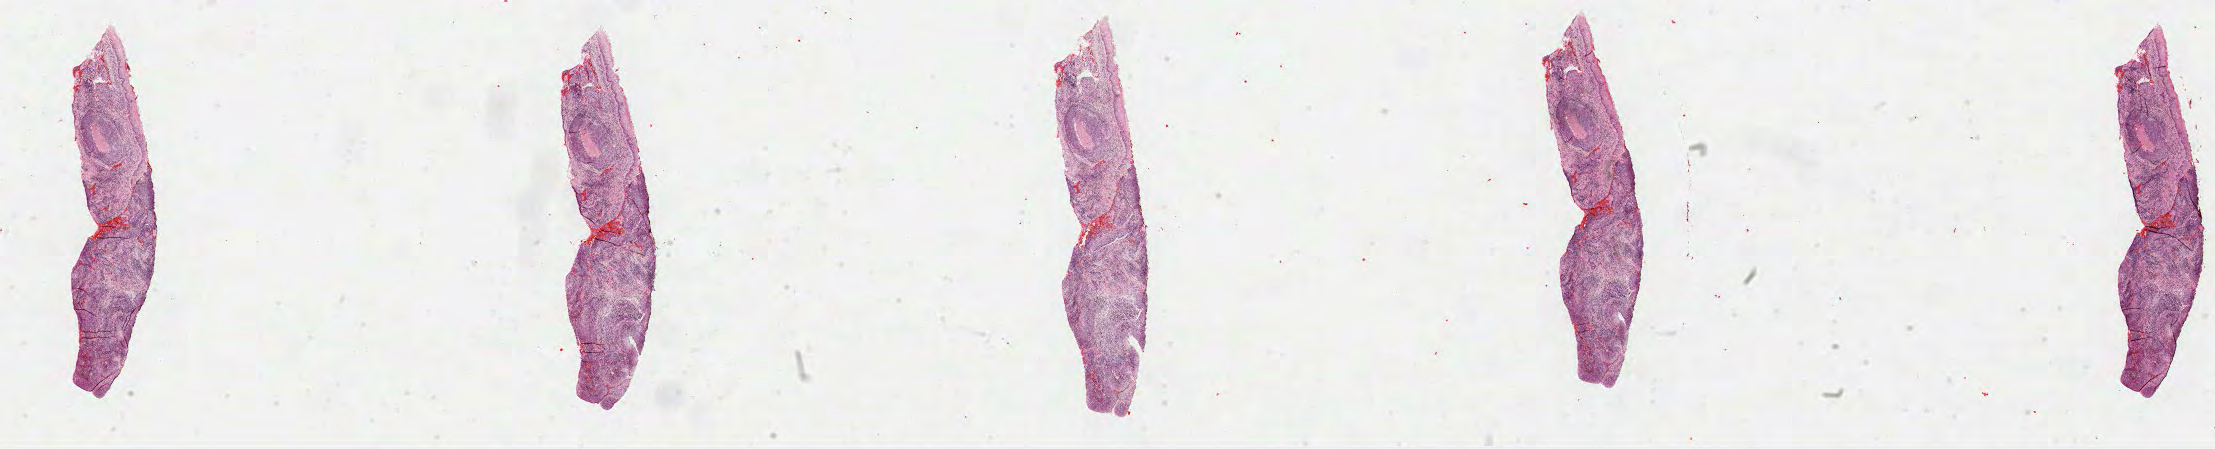
Digitized H&E-stained tissue section (whole slide), a low-resolution overview of the entire scanned area, about 35.7 x 7.2 mm, formalin-fixed paraffin-embedded (FFPE) diagnostic section, primary tumour sample from the cervix. Female patient; age at initial diagnosis 51 years. Histologic grade: G2 (moderately differentiated).
Diagnosis: Squamous cell carcinoma, large cell, nonkeratinizing, NOS (cervix uteri). FIGO stage: IIB.